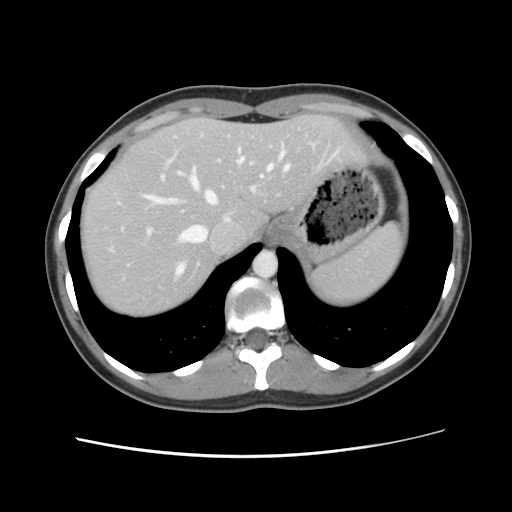
Contrast-enhanced abdominal CT, one axial slice. Slice 95 of 134 in the series (ordered by position). Intravenous contrast given. Soft-tissue window (W 400 / L 40 HU). 2.5 mm slice thickness. 512 × 512 image matrix, field of view 339 × 339 mm. Female patient, age 33 years. From the clinical record (not read from this slice): diagnosis: colorectal cancer liver metastases, imaged before liver resection; multiple liver metastases: yes; largest metastasis: 4.5 cm; chemotherapy before resection: no.
Annotated regions visible in this slice (expert manual segmentation):
- hepatic veins: bounding box [x1, y1, x2, y2] px = [142, 148, 290, 276]
- liver: [80, 115, 363, 318]
- planned liver remnant (the part of the liver to remain after resection): [80, 115, 364, 318]
- portal vein (with intrahepatic branches): [115, 200, 153, 239]